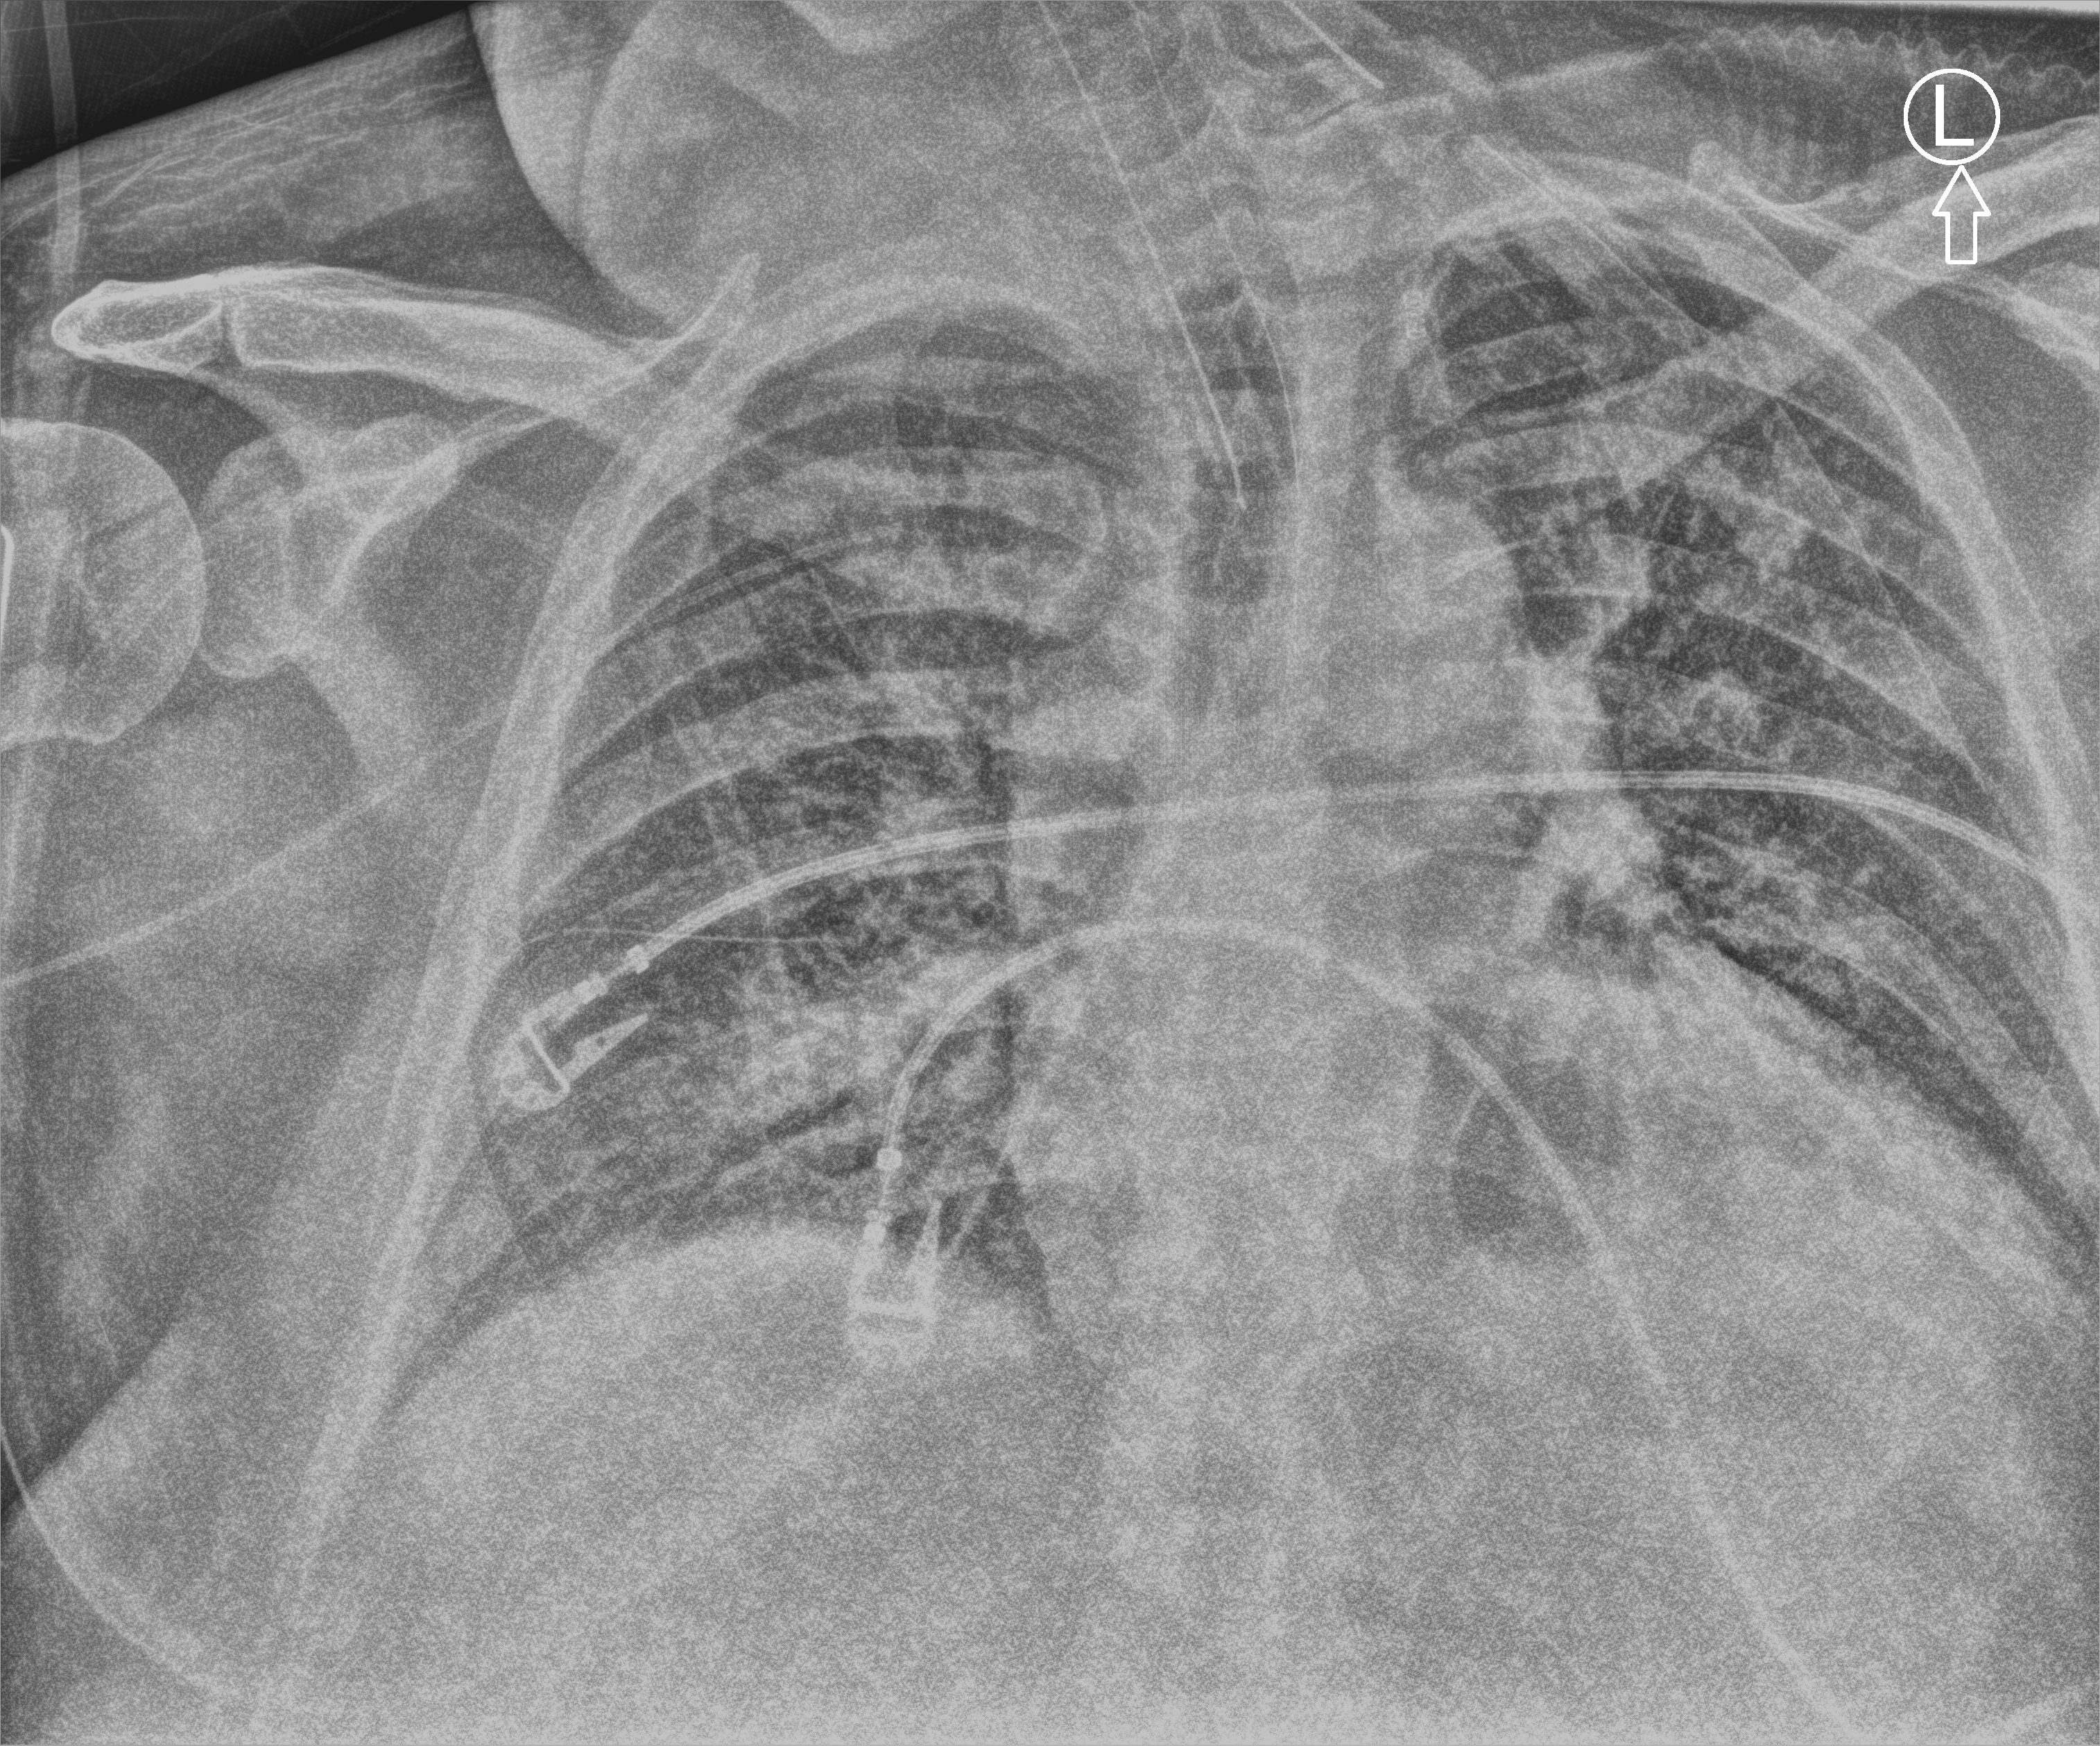
Bedside chest radiograph (computed radiography), anteroposterior (AP) projection. Patient hospitalised with COVID-19, aged 18–59 years.
Hospital-stay facts (about this admission, not read from this image; timing relative to this image not recorded):
- chronic kidney disease (admission record): no